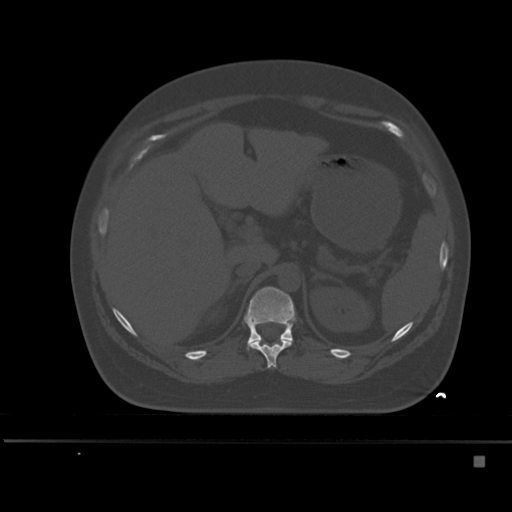
CT including the spine, one axial slice. Bone window (W 1800 / L 400 HU). 512 × 512 image matrix, field of view 404 × 404 mm. Patient: female, 33 years. Case-level facts recorded for this patient, not image findings: primary cancer: breast; vertebrae with lytic lesions (as recorded): T1.
Annotated regions visible in this slice (semi-automatic segmentation, software-assisted and operator-edited):
- T11 vertebra: bounding box <249,340,292,368> (left, top, right, bottom; pixels)
- T12 vertebra: <244,286,296,349>